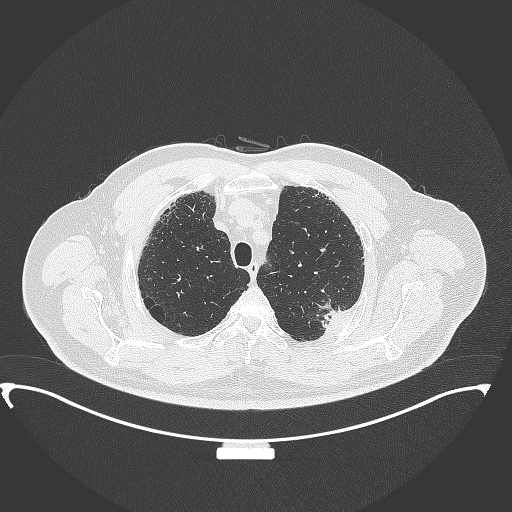
Chest CT, one axial slice. Slice 296 of 350 in the series (ordered by position). 120 kVp. Lung window (W 1500 / L -600 HU). 512 × 512 image matrix, field of view 459 × 459 mm. Male patient, age 64 years. Case-level facts recorded for this patient, not image findings: clinical TNM (as recorded): T1c N1 M1.
Outlined on this slice (rectangle marked by the reading radiologist):
- lung tumour (recorded histology: adenocarcinoma): bounding box [x1, y1, x2, y2] px = [315, 300, 354, 333]